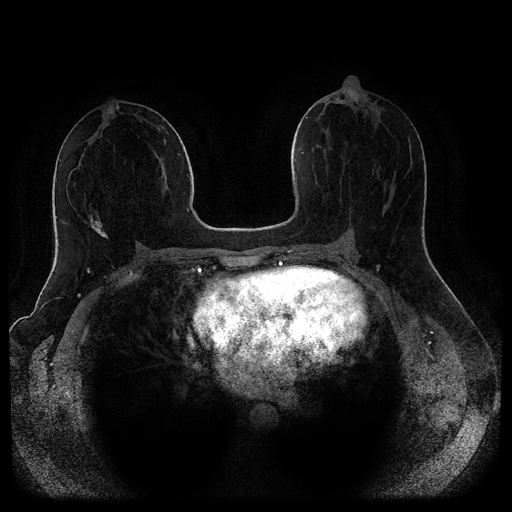
Breast MRI (dynamic contrast-enhanced, multi-phase), one axial slice; position 47 of 116 along the scan axis; dynamic contrast-enhanced series, time point 2 of 5 at this slice position (early post-contrast); 1.5 T; TE 2.6 ms, TR 5.3 ms; 512 × 512 image matrix, field of view 370 × 370 mm. Female patient, age 44 years.
Annotated regions visible in this slice (semi-automatic segmentation, software-assisted and operator-edited):
- breast lesion (labelled benign in the annotation): box from (x=90, y=217) to (x=108, y=239) px